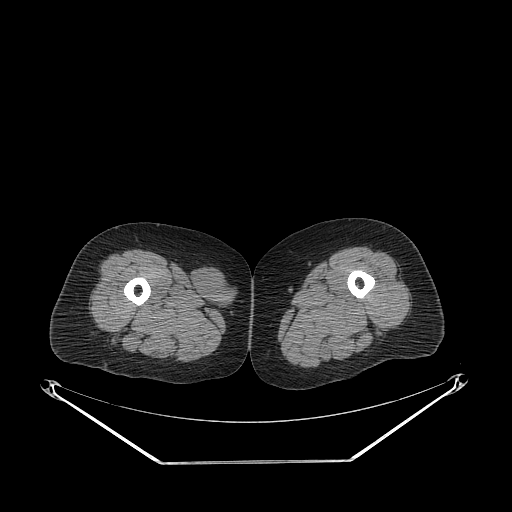
CT of an extremity soft-tissue mass (from a PET/CT study), one axial slice. Position 239 of 311 along the scan axis. Reconstruction kernel STANDARD. 140 kVp. Soft-tissue window (W 400 / L 40 HU). 3.75 mm slice thickness. 512 × 512 image matrix, field of view 500 × 500 mm. Female patient. Case-level facts recorded for this patient, not image findings: histological type: leiomyosarcoma; grade: intermediate; site of the primary tumour: parascapusular.
Annotated regions visible in this slice (expert contour drawn on MRI and transferred to this co-registered scan by the dataset authors):
- gross tumour volume including surrounding oedema: bounding box <190,265,234,311> (left, top, right, bottom; pixels)
- gross tumour volume (mass): <192,265,229,309>